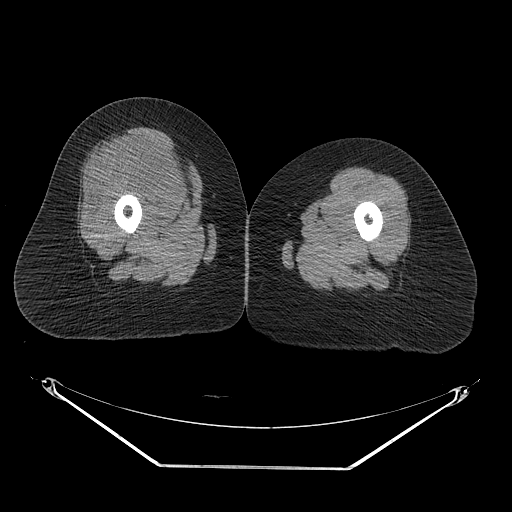
CT of an extremity soft-tissue mass (from a PET/CT study), one axial slice. Position 29 of 267 along the scan axis. 140 kVp. Soft-tissue window (W 400 / L 40 HU). 3.75 mm slice thickness. 512 × 512 image matrix. Female patient. From the clinical record (not read from this slice): histological type: malignant solitary fibrous tumor; grade: intermediate; site of the primary tumour: right thigh.
Annotated regions visible in this slice (expert contour drawn on MRI and transferred to this co-registered scan by the dataset authors):
- gross tumour volume including surrounding oedema: bounding box (x1, y1, x2, y2) in pixels: (98, 132, 202, 218)
- gross tumour volume (mass): (101, 132, 199, 211)